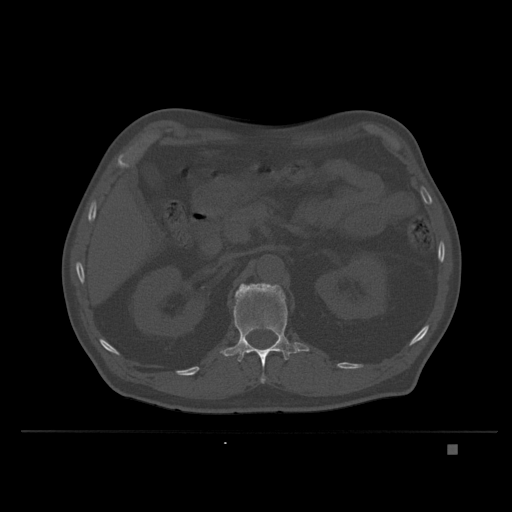
CT including the spine, one axial slice. Position 138 of 435 along the scan axis. Bone window (W 1800 / L 400 HU). 1.5 mm slice thickness. 512 × 512 image matrix. Male patient, age 73 years. Case-level facts recorded for this patient, not image findings: primary cancer: skin.
Outlined on this slice (semi-automatically segmented with operator editing):
- L1 vertebra: box from (x=220, y=283) to (x=310, y=384) px